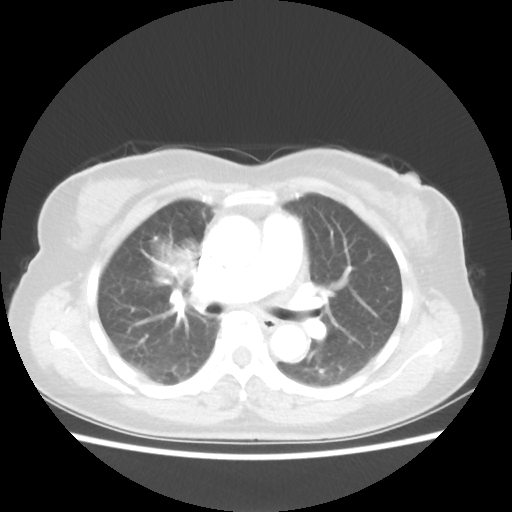
Chest CT, one axial slice; position 32 of 55 along the scan axis; reconstruction kernel STANDARD; 80 kVp; lung window (W 1500 / L -600 HU); 512 × 512 image matrix, field of view 337 × 337 mm. Patient: female, 62 years. From the clinical record (not read from this slice): clinical TNM (as recorded): T4 N3 M0.
Structures marked on this image (rectangle marked by the reading radiologist):
- lung tumour (recorded histology: squamous cell carcinoma): box from (x=139, y=226) to (x=217, y=301) px